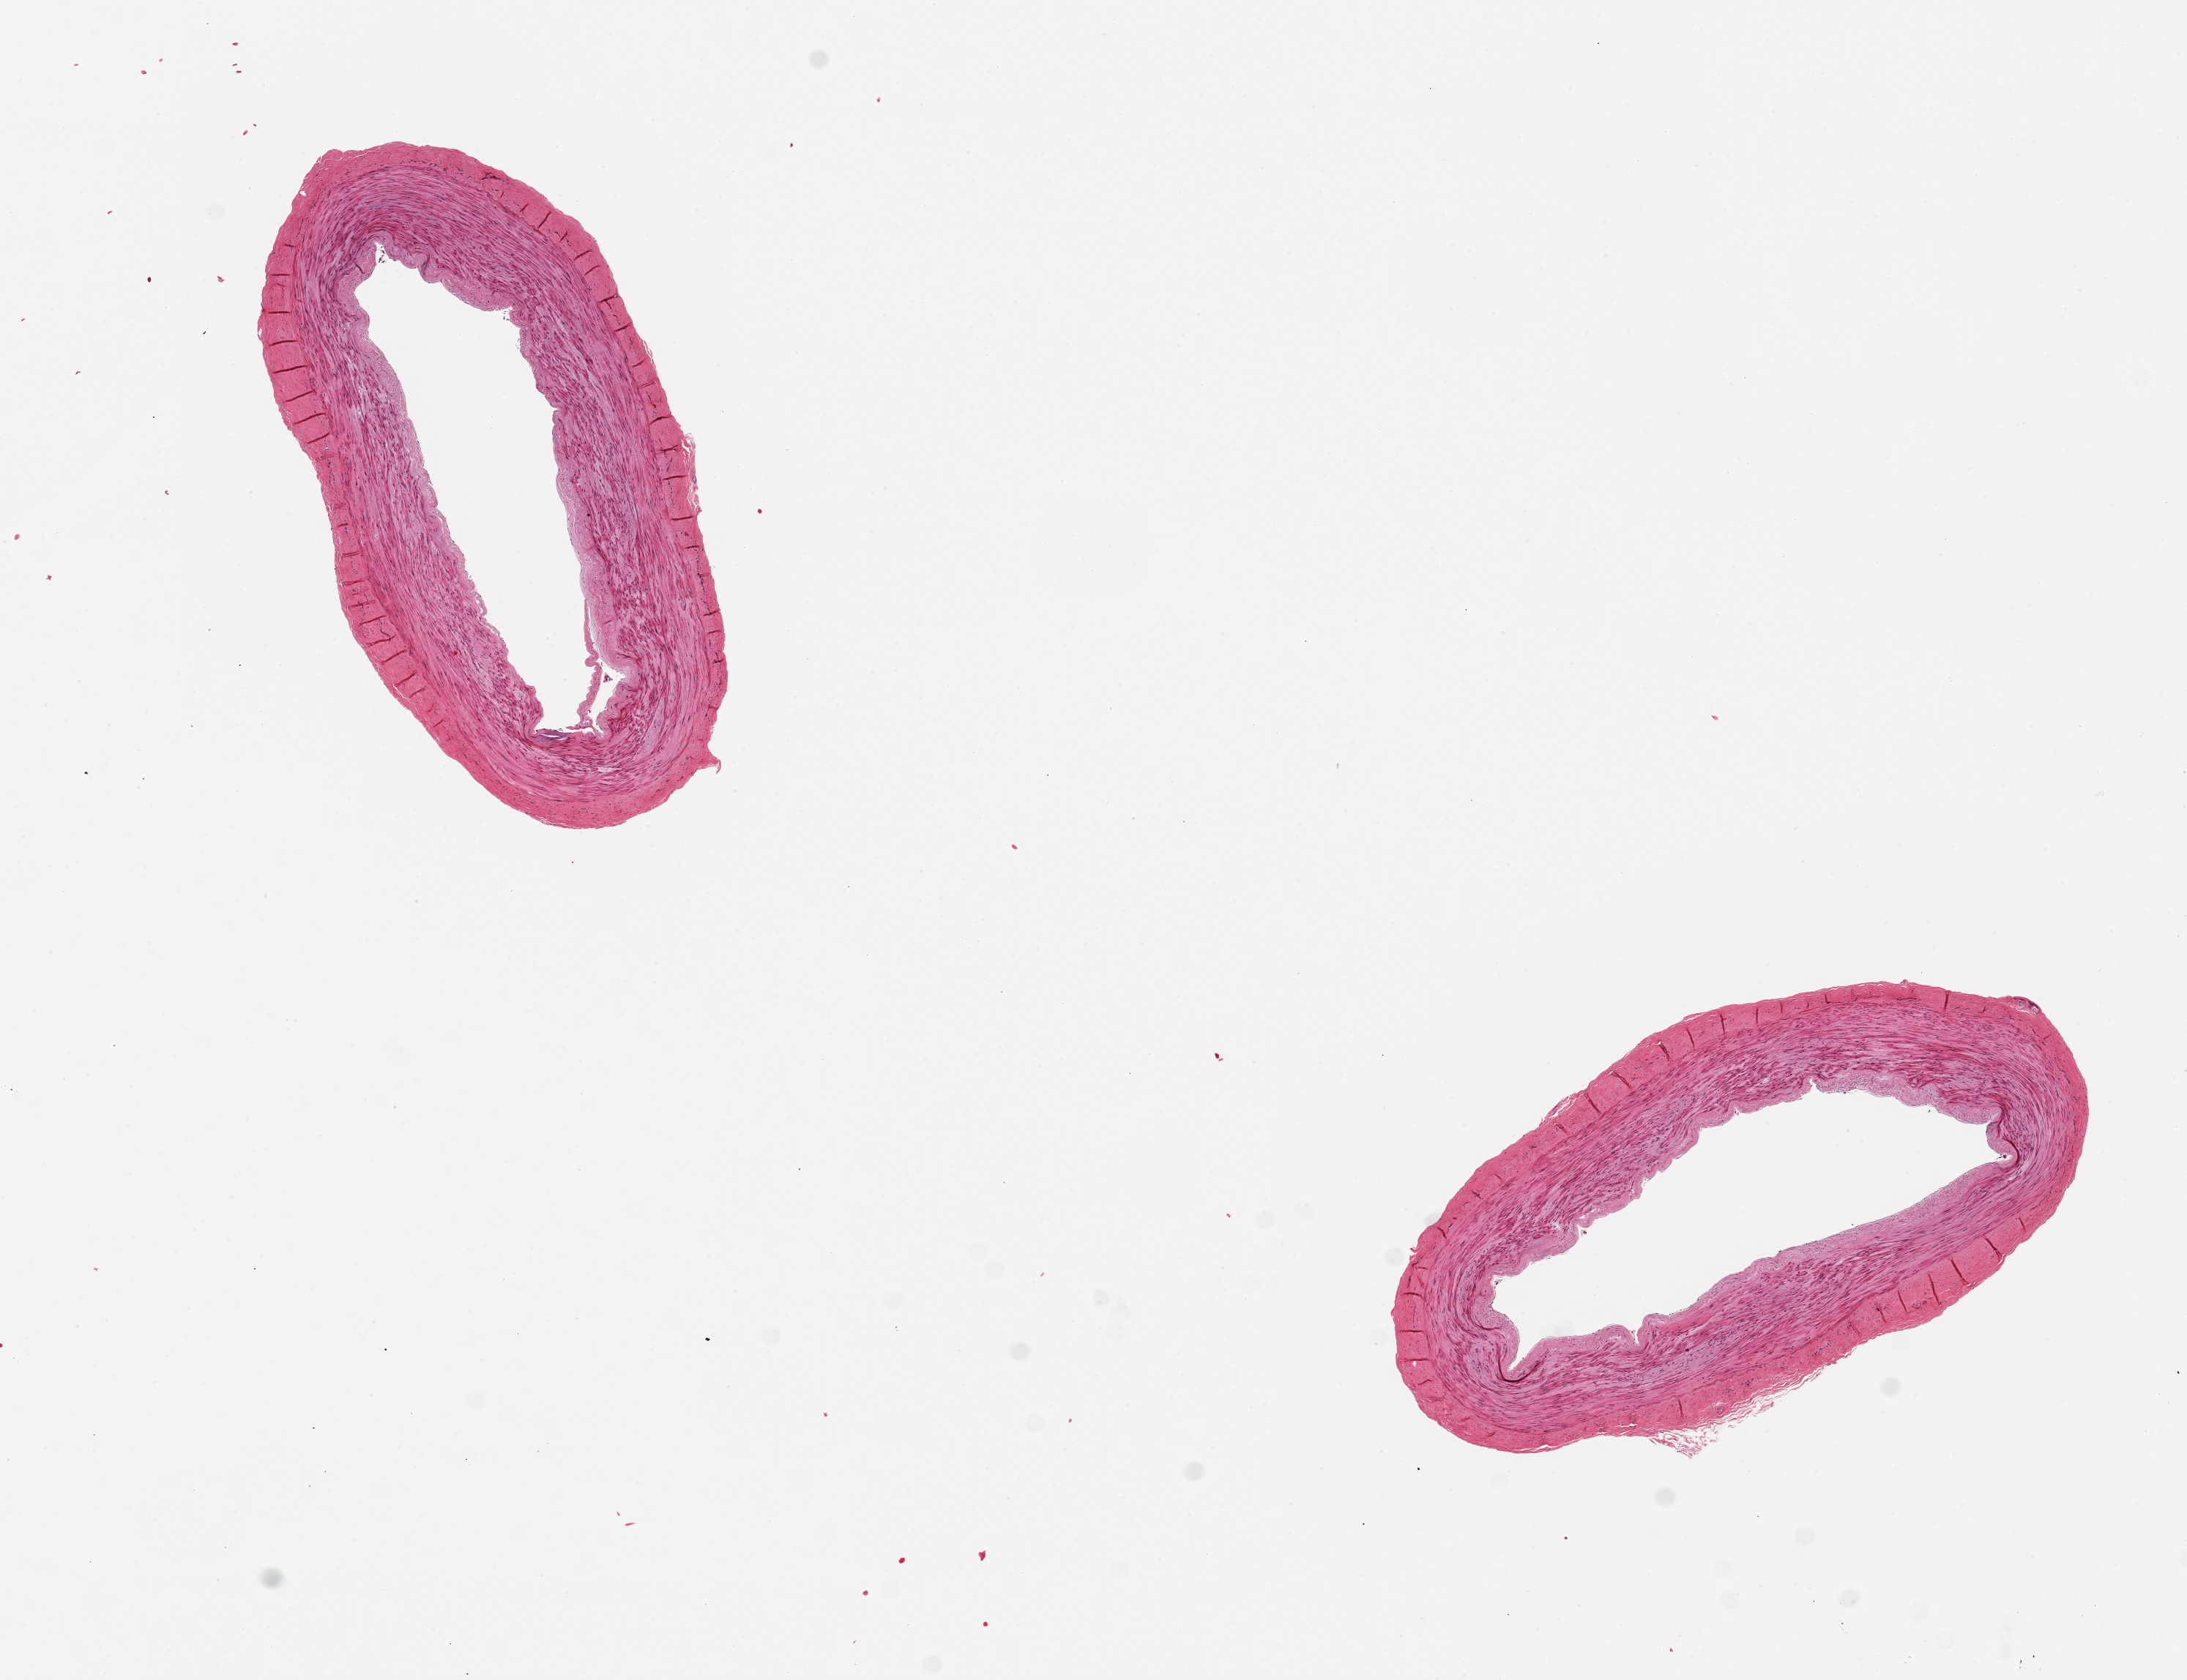
Digitized H&E-stained section — whole scanned area (about 11.8 x 9.1 mm) shown as a low-resolution overview; PAXgene-fixed, paraffin-embedded tissue; sampled site (target tissue): tibial artery; tissue donor sample. Male donor.
Pathologist's review note for this sample: 2 pieces 4x2 & 4x2mm; good clean specimens.